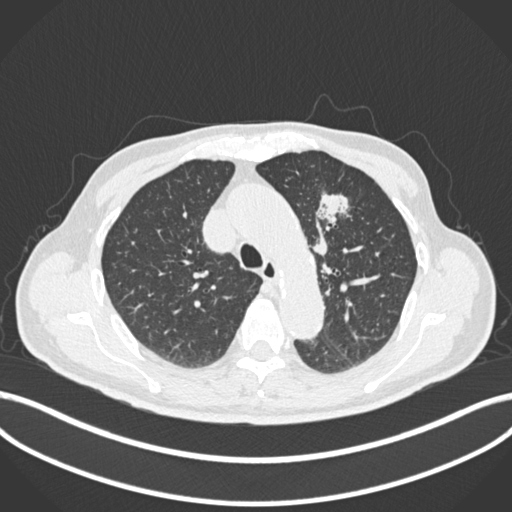
Chest CT, one axial slice. Position 180 of 261 along the scan axis. 120 kVp. Lung window (W 1500 / L -600 HU). 1 mm slice thickness. 512 × 512 image matrix, field of view 400 × 400 mm. Patient: male, 74 years. From the clinical record (not read from this slice): clinical TNM (as recorded): T2b N0 M1c.
Structures marked on this image (rectangle marked by the reading radiologist):
- lung tumour (recorded histology: adenocarcinoma): bounding box <312,184,357,229> (left, top, right, bottom; pixels)